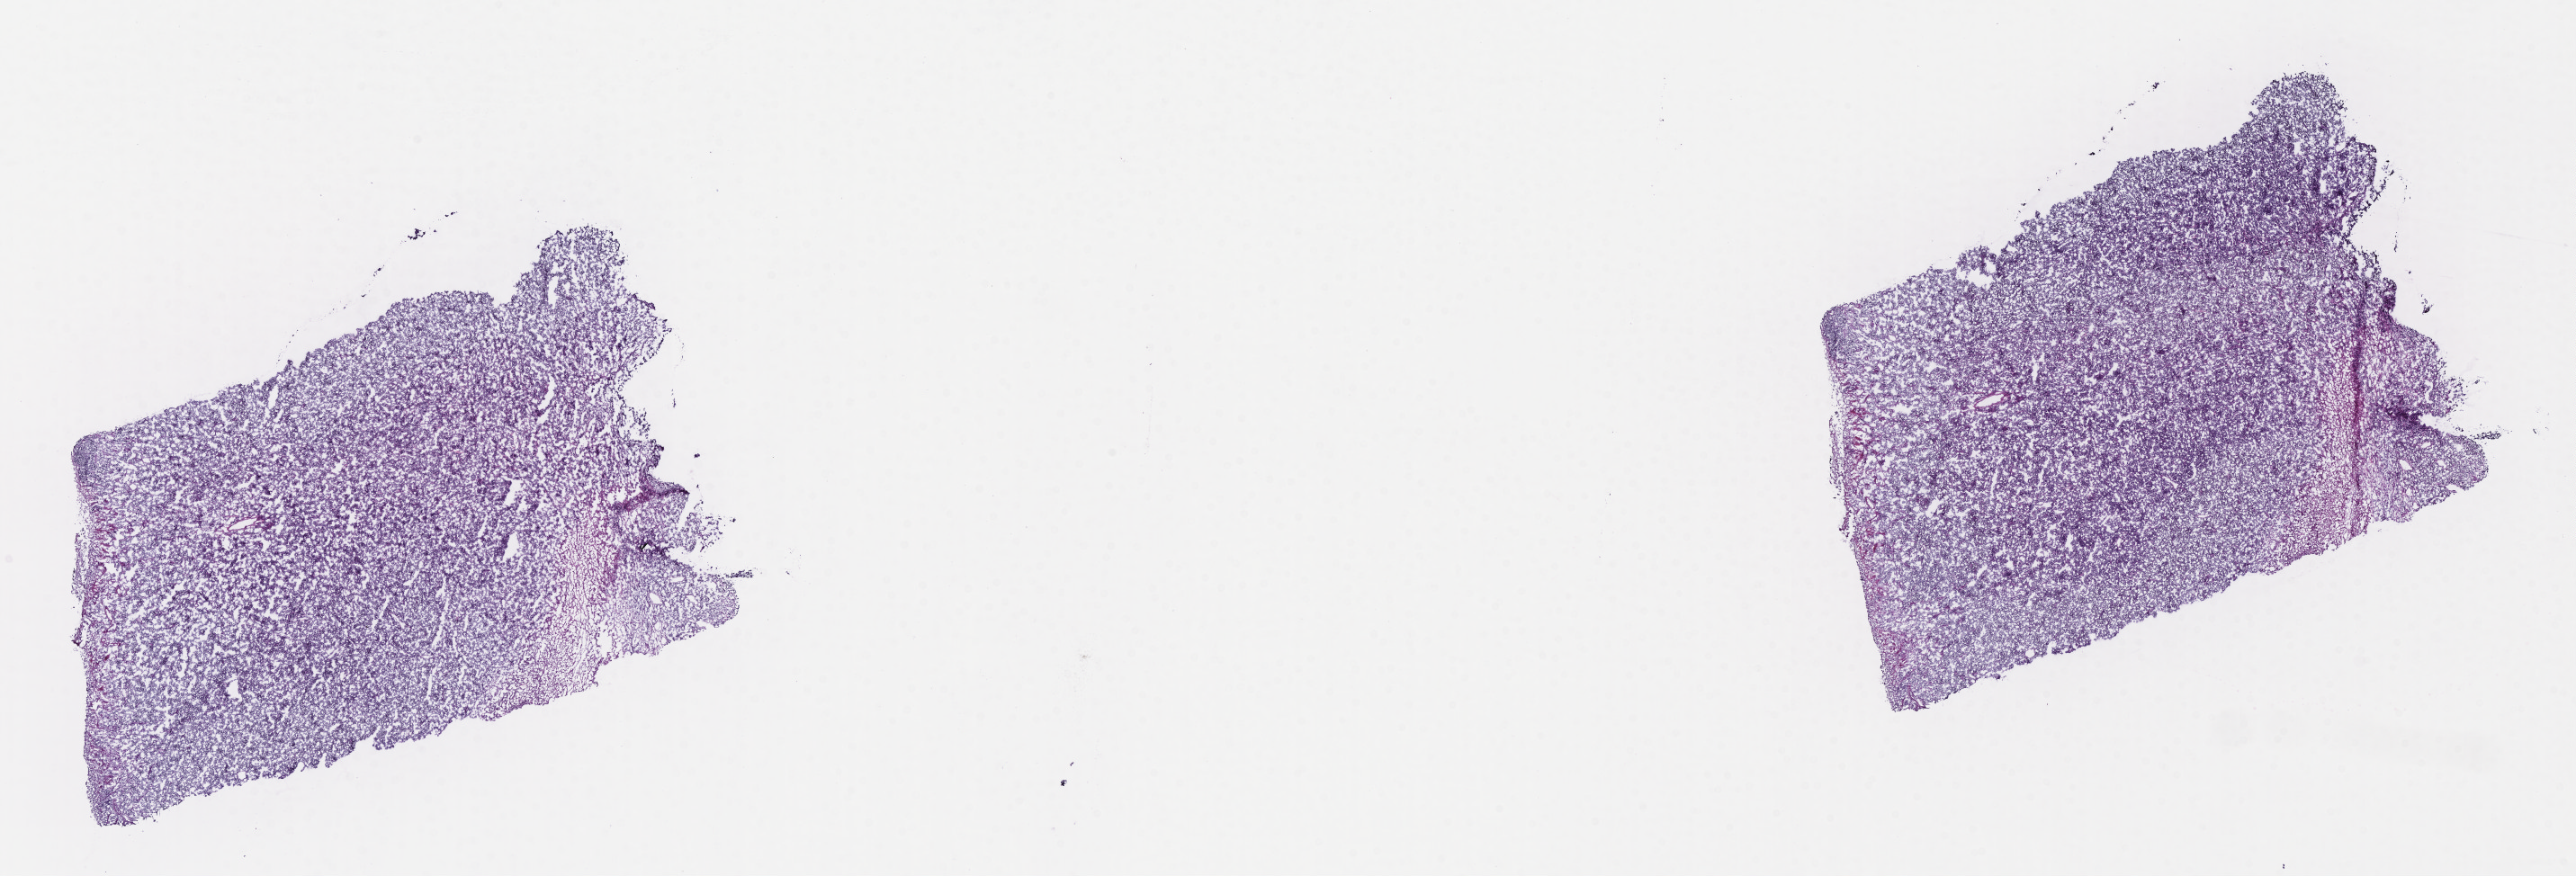
Hematoxylin and eosin (H&E) whole-slide image, a low-resolution overview of the entire scanned area, about 23.1 x 7.9 mm; frozen section (tissue freezing medium); specimen: primary tumor; site: colon. Male patient, 14 years old. Slide review estimates, as recorded: tumor cells 85%, tumor nuclei 90%, stromal cells 10%, necrosis 0%, normal cells 5%. Infiltration values recorded for this section: lymphocyte infiltration 80%, monocyte infiltration 15%, neutrophil infiltration 0%.
- histologic diagnosis: Burkitt lymphoma, NOS
- Ann Arbor stage (patient): Stage IV